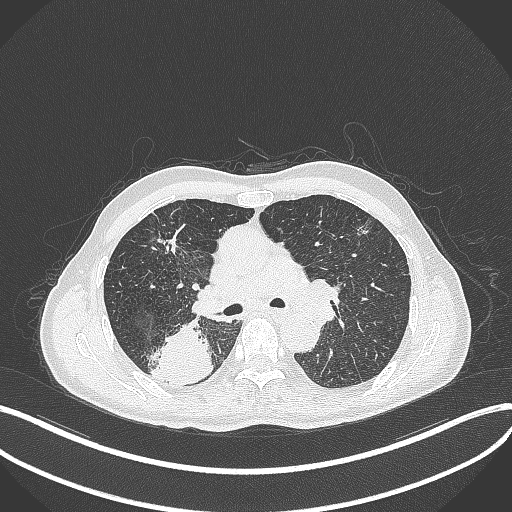
Chest CT, one axial slice; slice 281 of 428 in the series (ordered by position); reconstruction kernel B70f; lung window (W 1500 / L -600 HU); 1 mm slice thickness; 512 × 512 image matrix, field of view 400 × 400 mm. Patient: male, 79 years. From the clinical record (not read from this slice): clinical TNM (as recorded): T3 N0 M0.
Annotated regions visible in this slice (bounding box drawn by a radiologist):
- lung tumour (recorded histology: adenocarcinoma): bounding box [x1, y1, x2, y2] px = [152, 319, 214, 388]